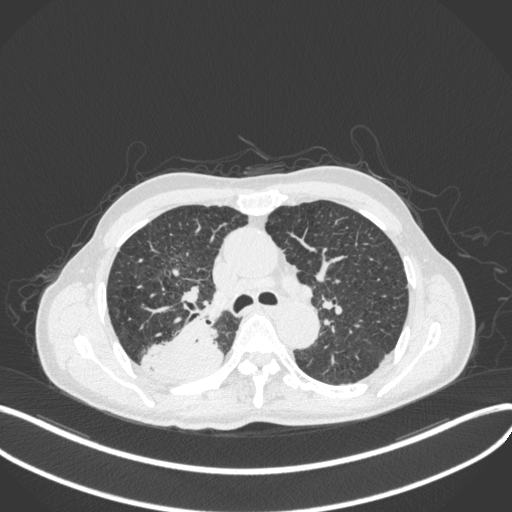
Chest CT, one axial slice; slice 300 of 423 in the series (ordered by position); 120 kVp; lung window (W 1500 / L -600 HU); 1 mm slice thickness; 512 × 512 image matrix, field of view 400 × 400 mm. Patient: male, 79 years. Case-level facts recorded for this patient, not image findings: clinical TNM (as recorded): T3 N0 M0.
Structures marked on this image (bounding box drawn by a radiologist):
- lung tumour (recorded histology: adenocarcinoma): bounding box [x1, y1, x2, y2] px = [137, 311, 224, 387]